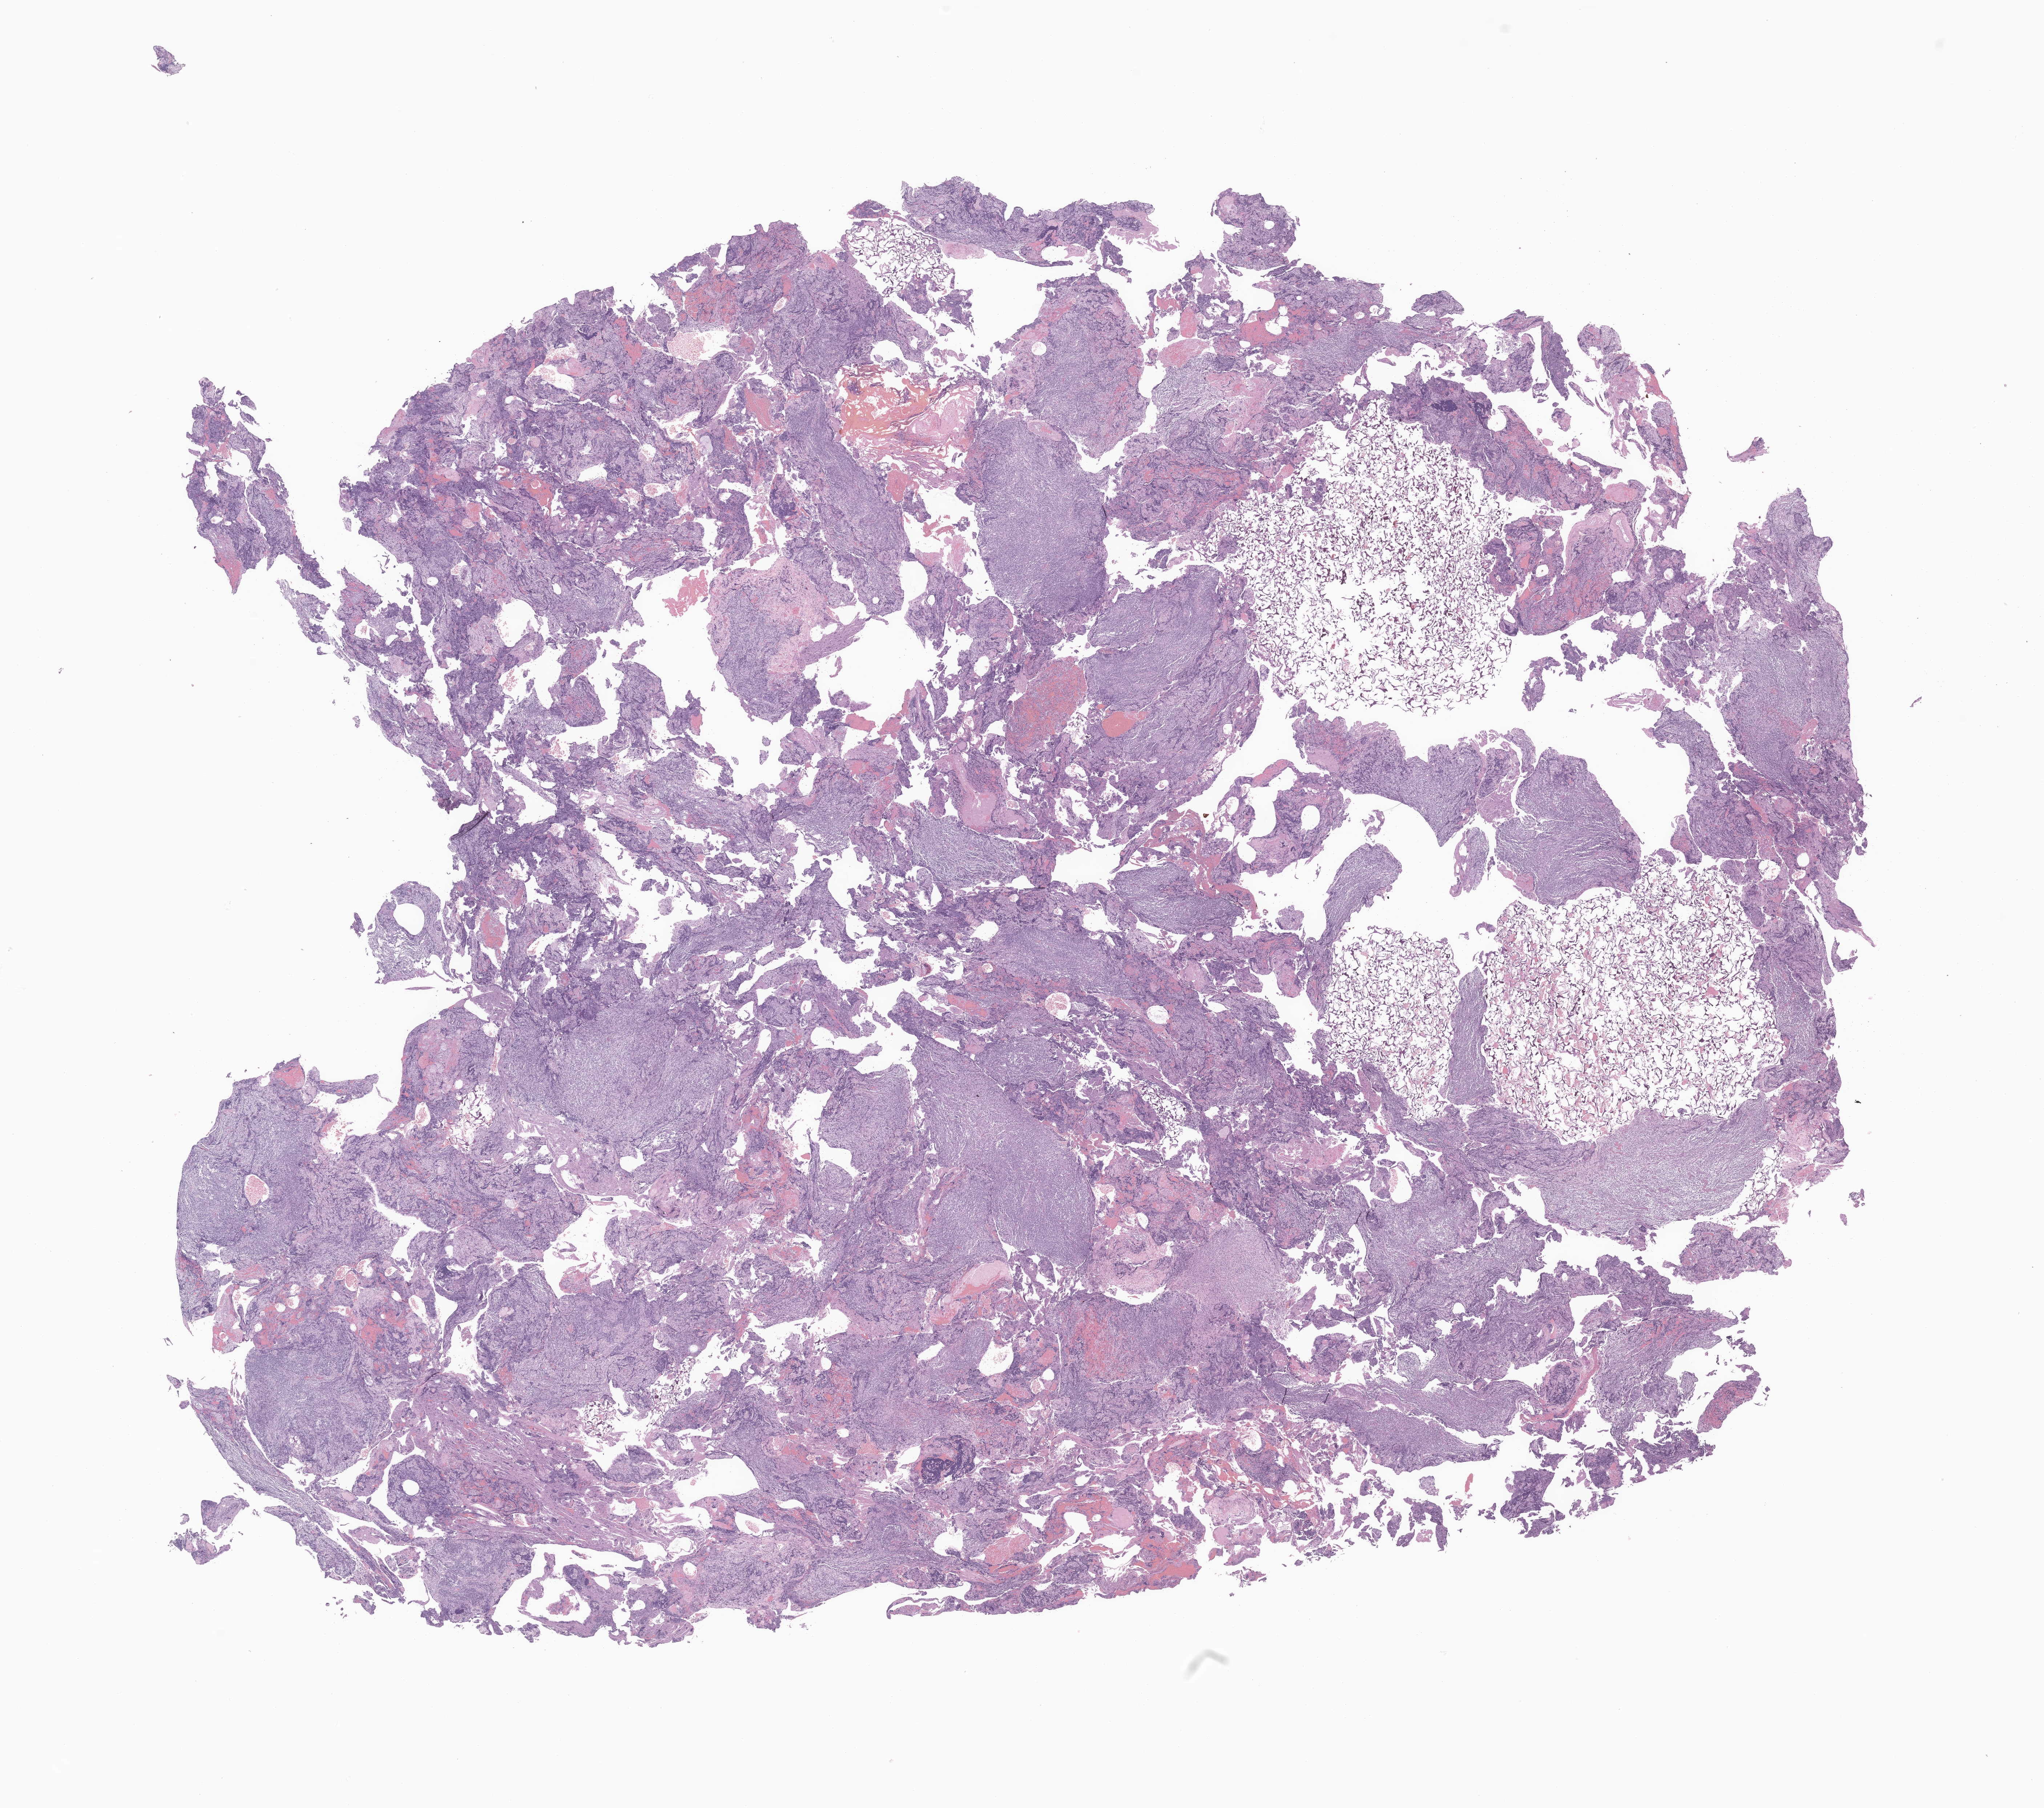
Digitized haematoxylin and eosin-stained section of tumor tissue from the brain, a low-resolution overview of the entire scanned area, about 23.7 x 21.0 mm; FFPE section. Male patient, age 305 days.
- diagnosis (ICD-O-3 morphology term): Medulloblastoma, NOS